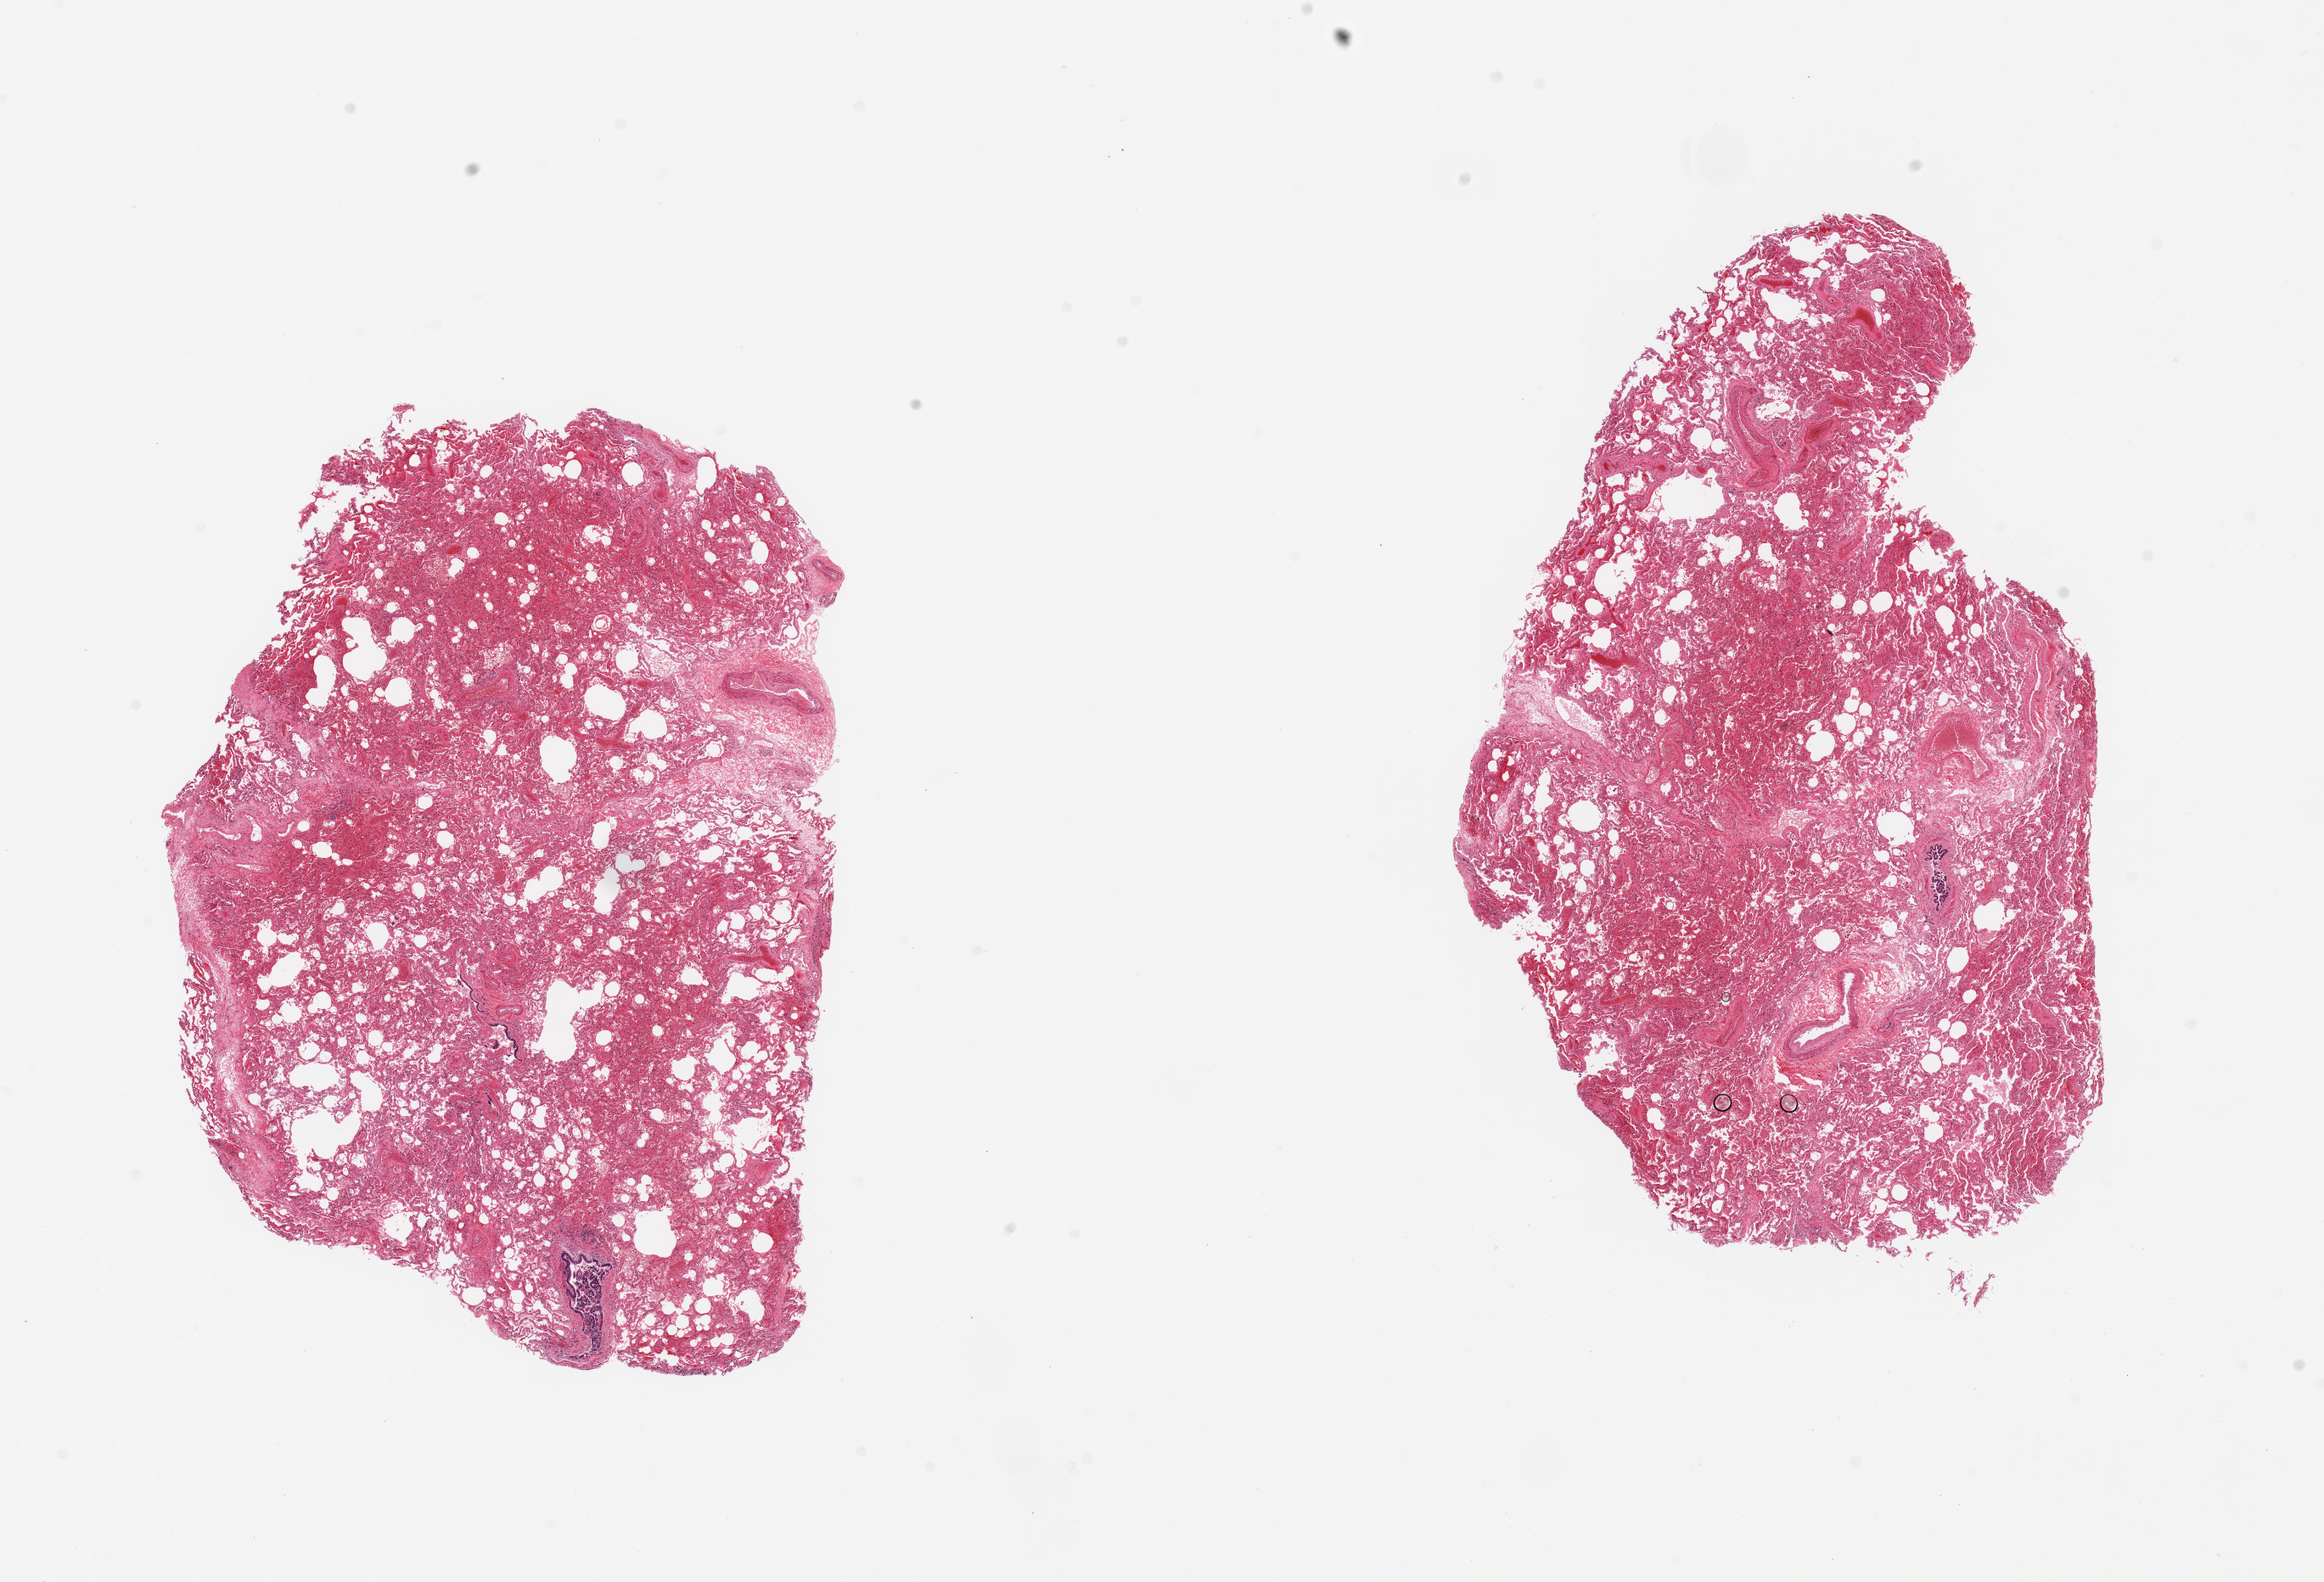
H&E whole-slide image, brightfield — shown as a low-resolution overview of the whole scanned area (about 21.7 x 14.7 mm); PAXgene-fixed, paraffin-embedded tissue; sampled site (target tissue): lung; tissue donor sample.
- reviewer comment on this tissue sample: 2 pieces; focal congestion, hemorrhage & emphysema